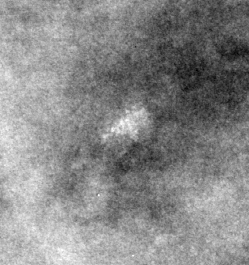
Crop from a digitized film mammogram around one marked abnormality, right breast, CC view.
Calcifications, morphology punctate / amorphous, distribution clustered; BI-RADS assessment category 4; pathology result (as recorded, not read from the image): benign.